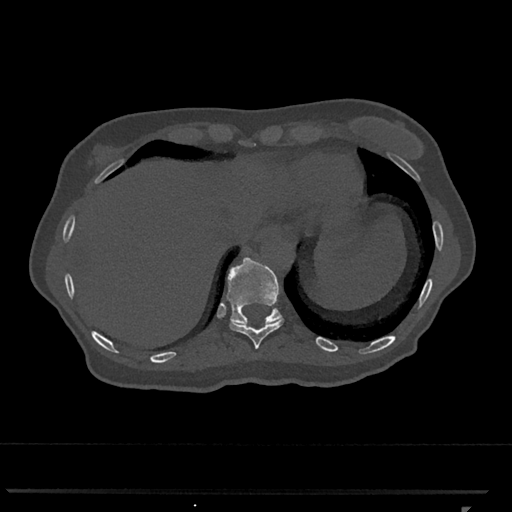
CT including the spine, one axial slice. Position 549 of 793 along the scan axis. Reconstruction kernel Br40s/3. 120 kVp. Bone window (W 1800 / L 400 HU). 0.5 mm slice thickness. 512 × 512 image matrix, field of view 380 × 380 mm. Female patient, age 62 years. Case-level facts recorded for this patient, not image findings: primary cancer: renal.
Structures marked on this image (semi-automatically segmented with operator editing):
- T10 vertebra: bounding box <230,318,283,349> (left, top, right, bottom; pixels)
- T11 vertebra: <226,257,283,325>